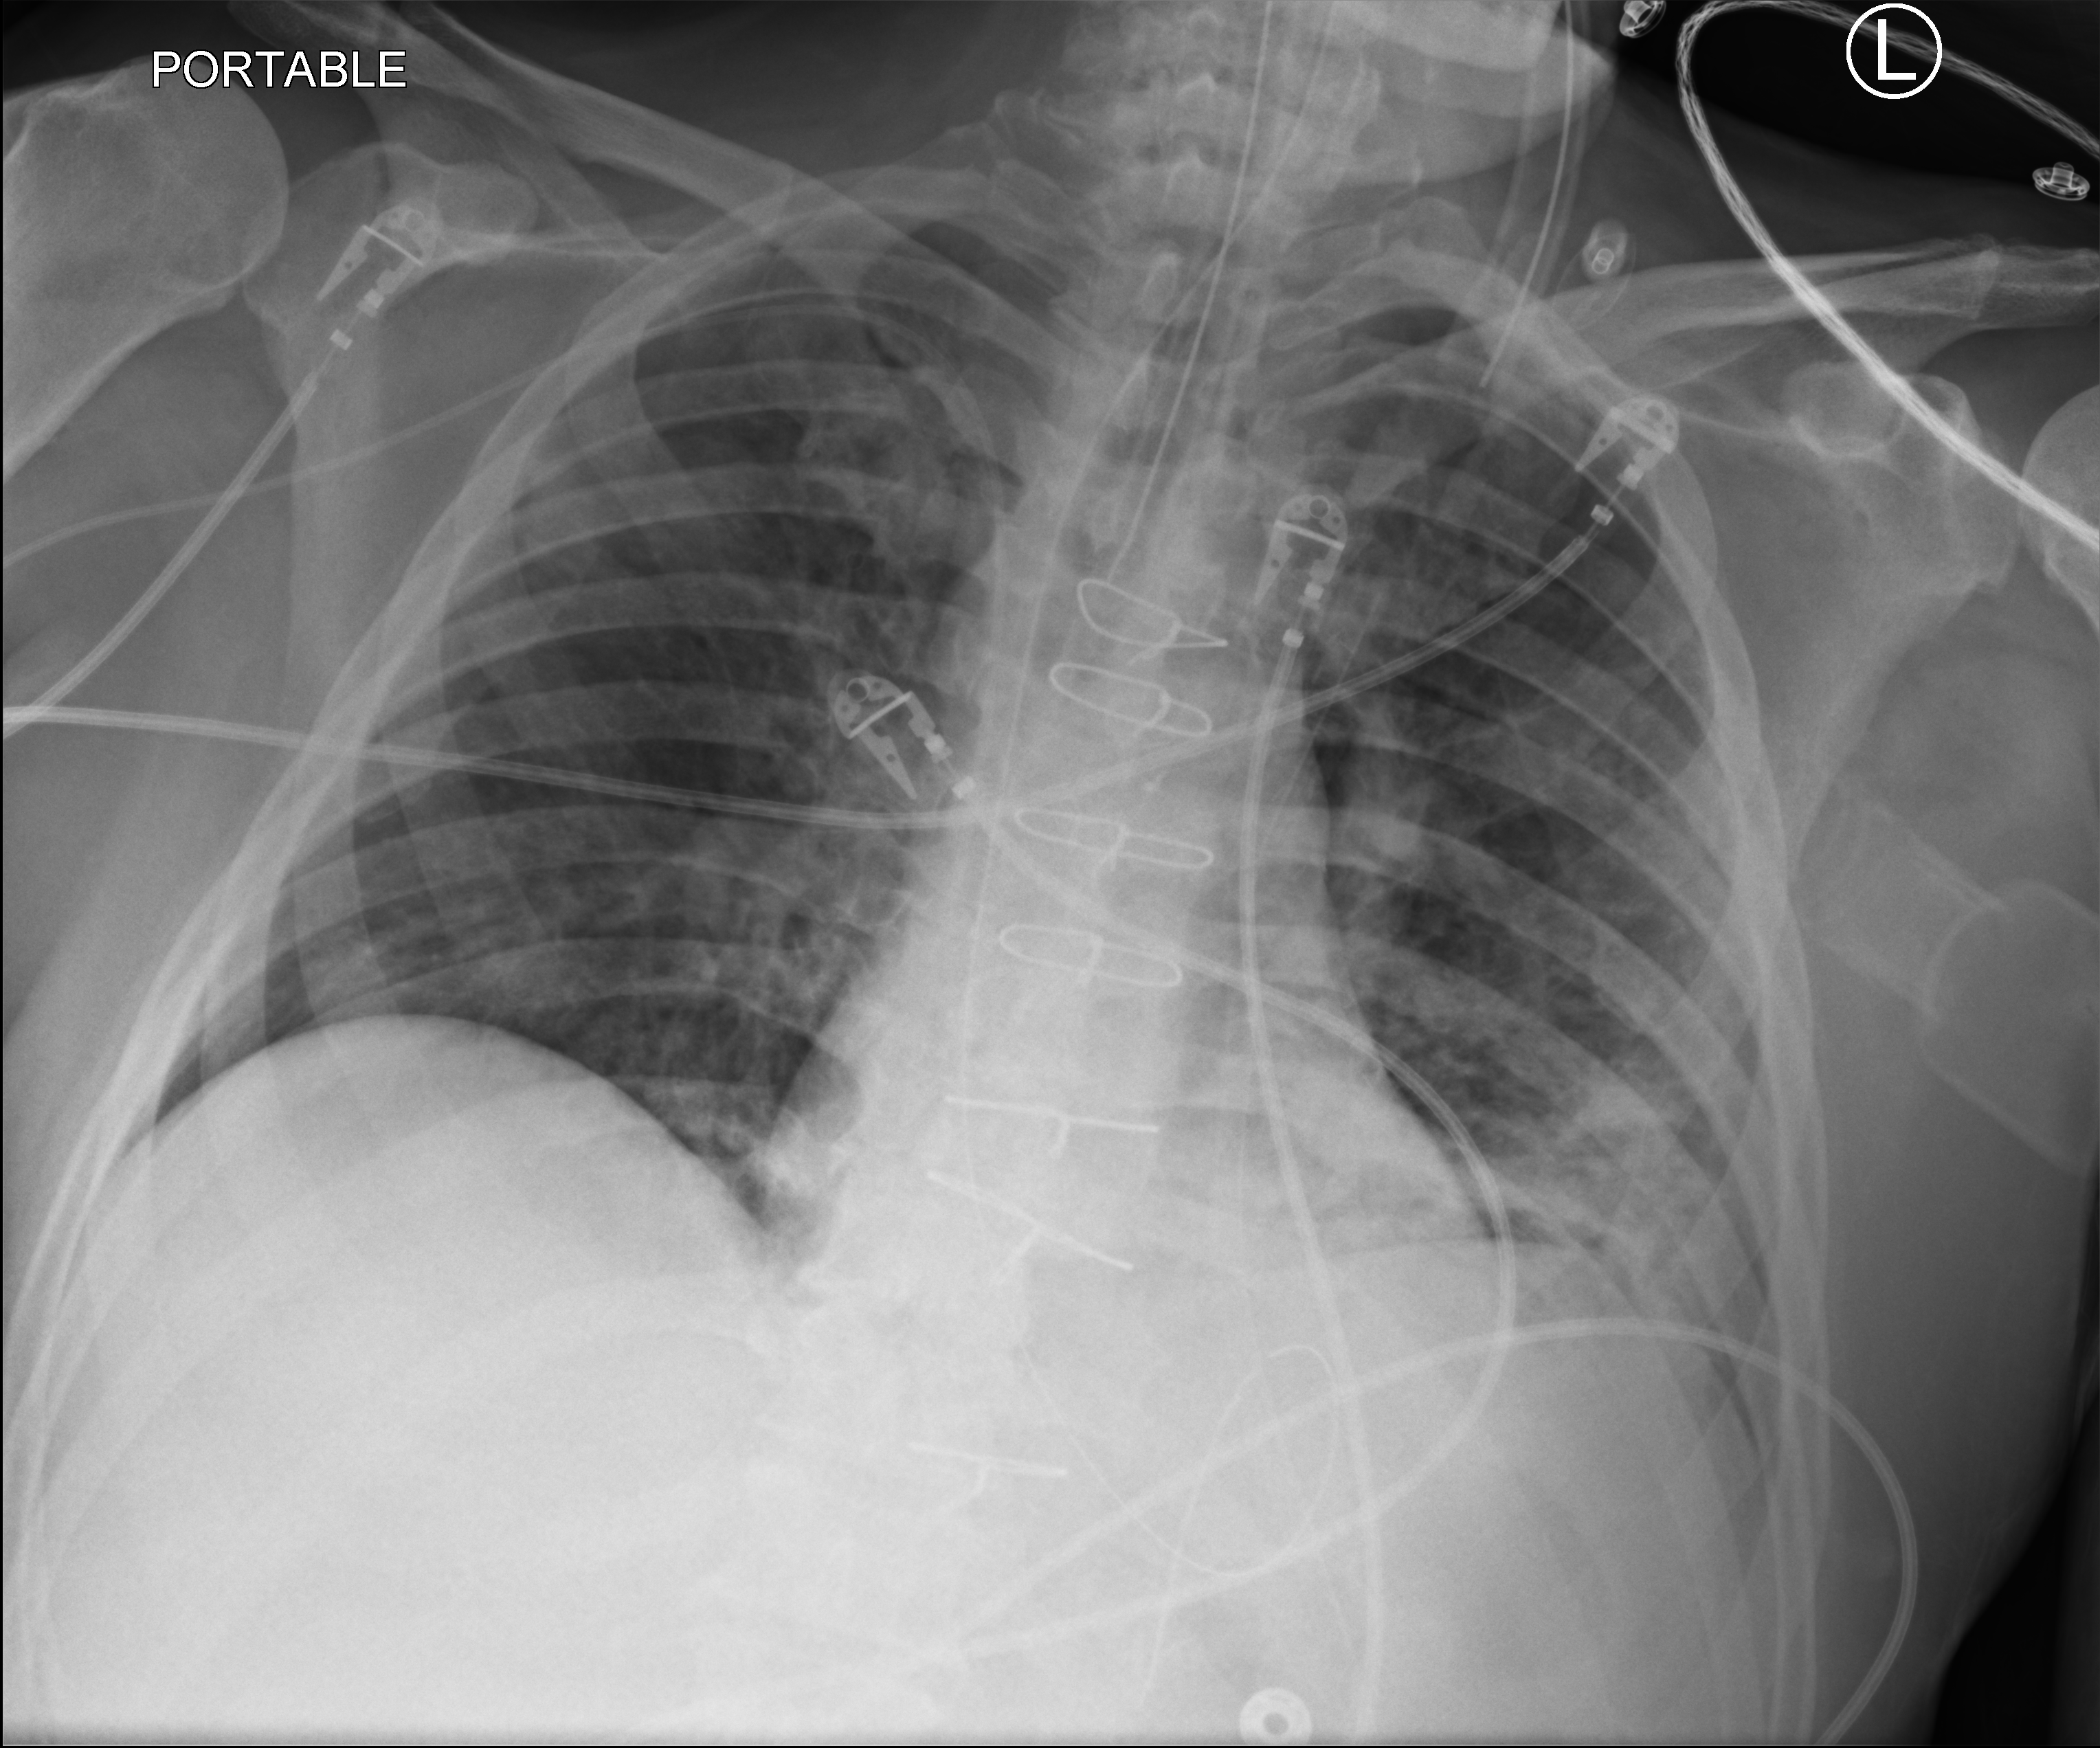
Chest X-ray (portable), anteroposterior (AP) projection. Male patient hospitalised with COVID-19, age 60–74 years.
Hospital-stay facts (about this admission, not read from this image; timing relative to this image not recorded): admitted to intensive care during this hospital stay: yes; mechanically ventilated during this hospital stay: yes.